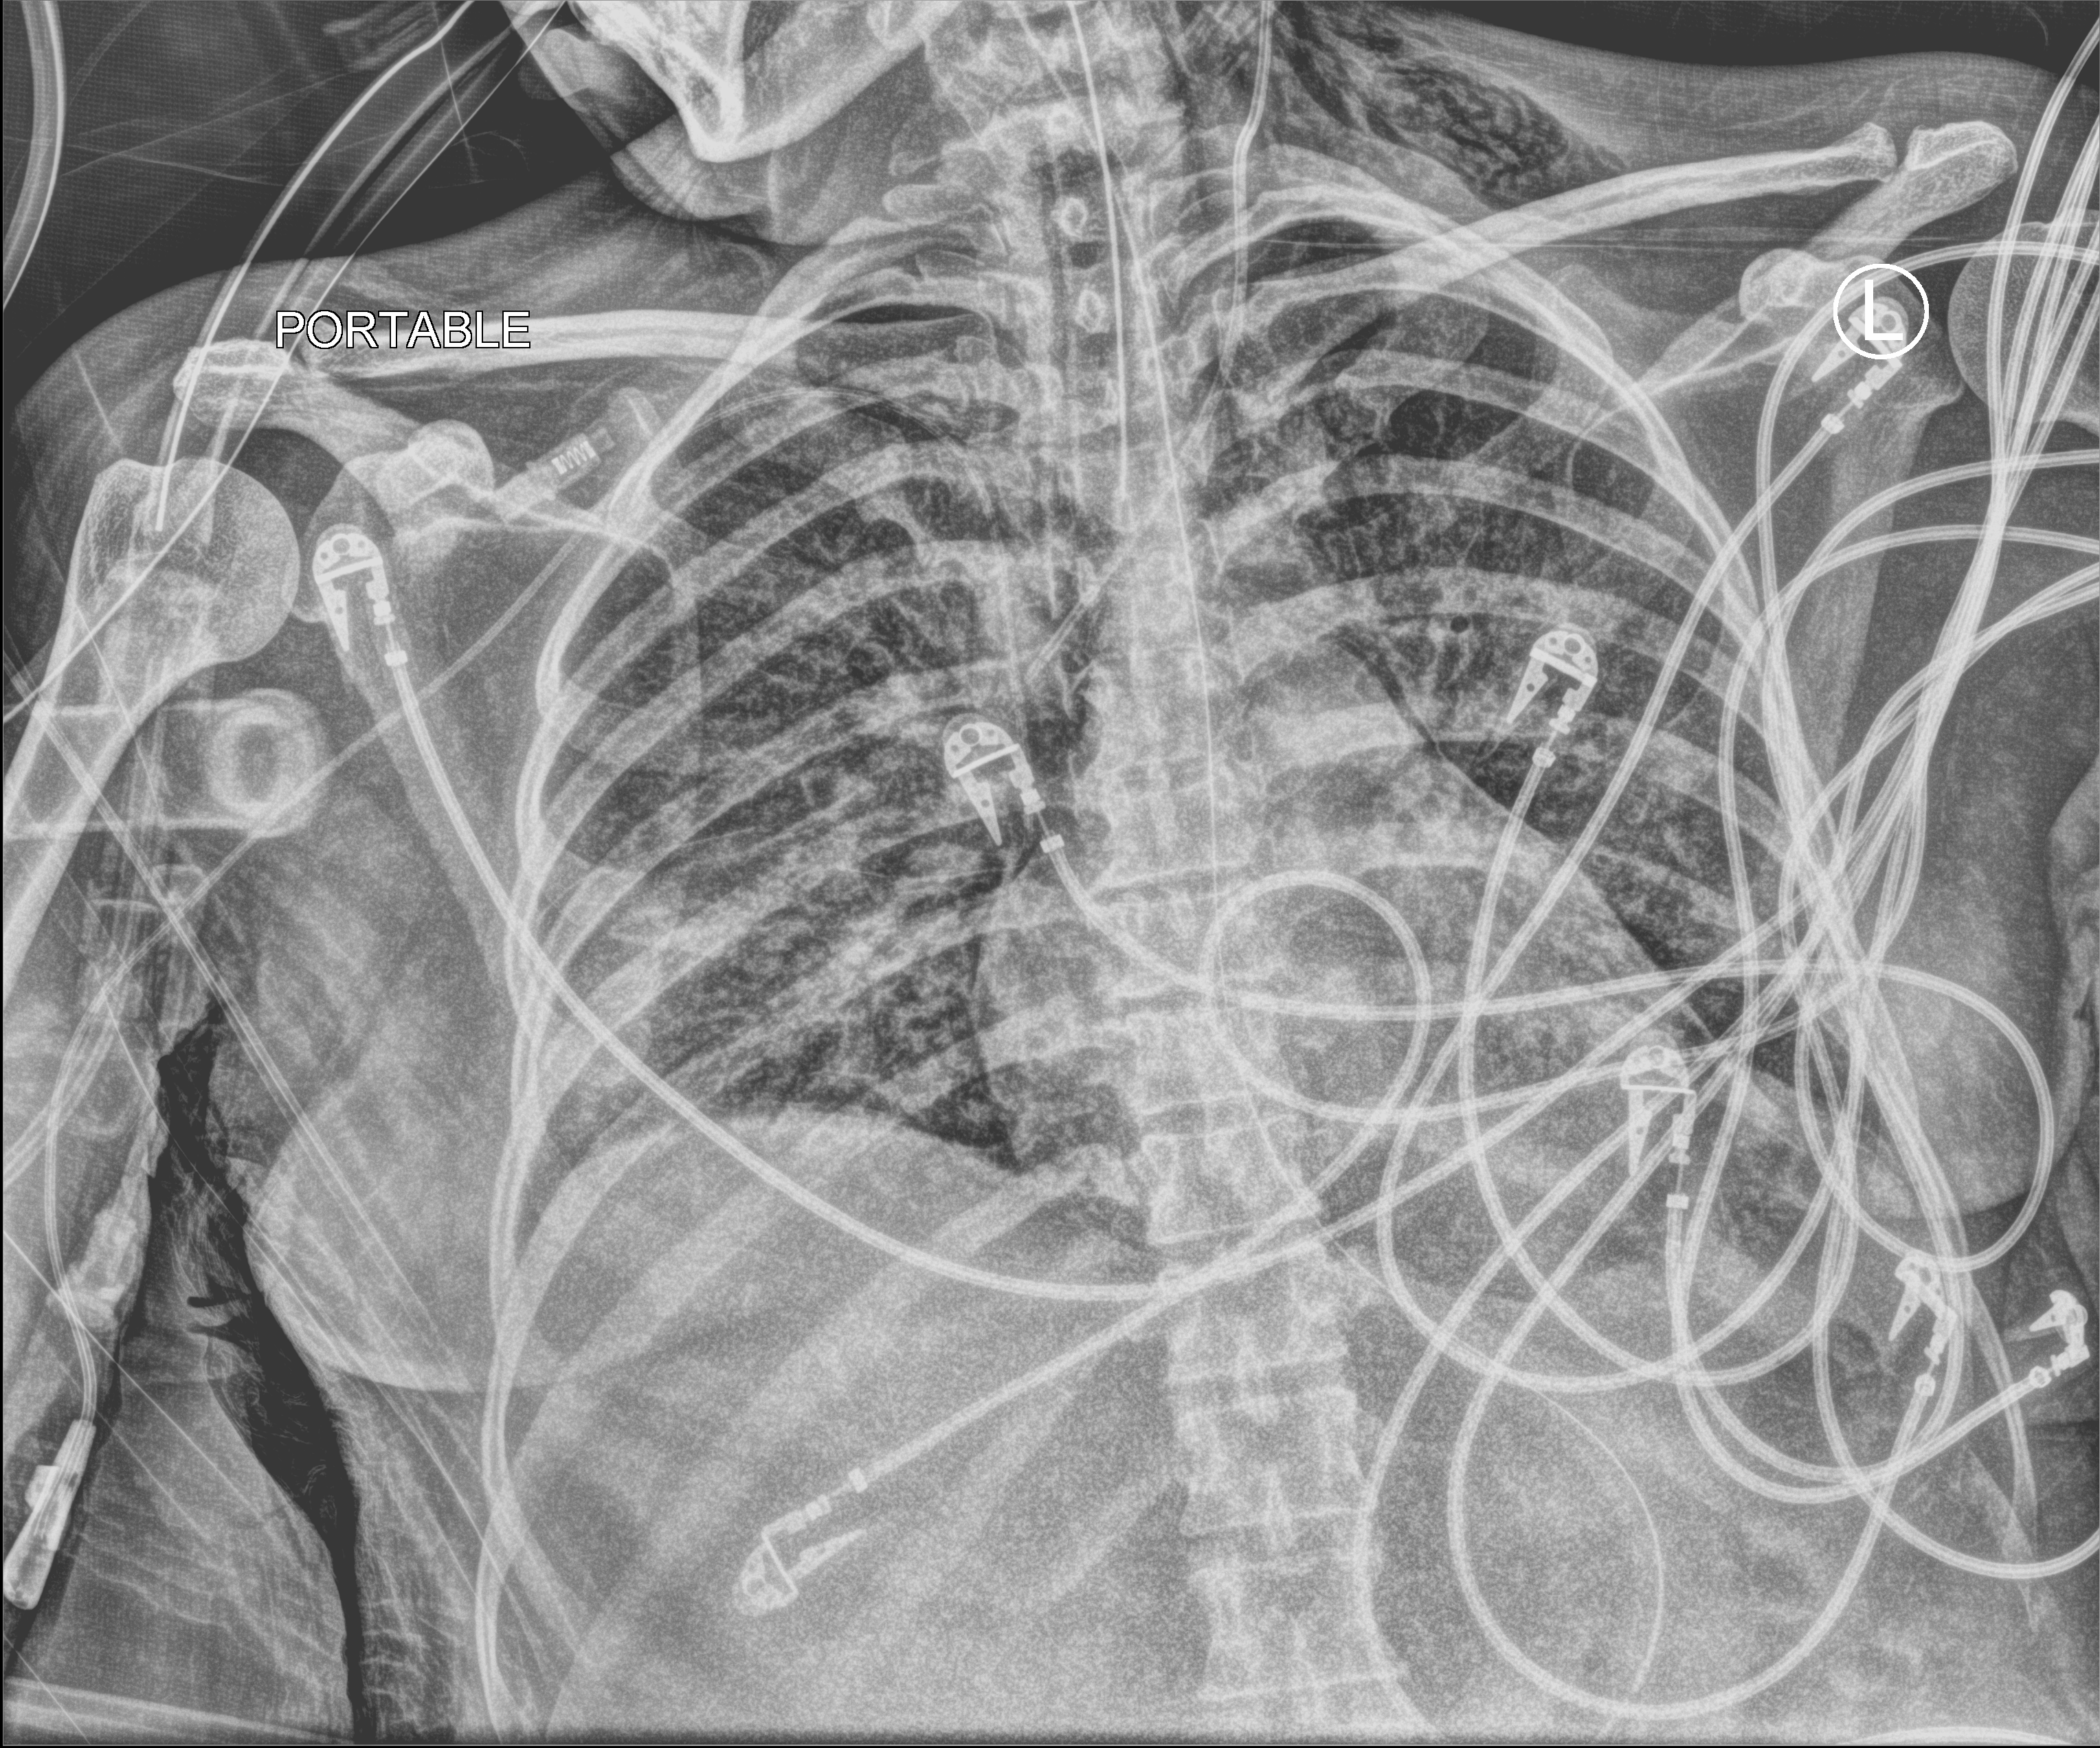
Portable chest radiograph. Female patient hospitalised with COVID-19, age 18–59 years.
Hospital-stay facts (about this admission, not read from this image; timing relative to this image not recorded): length of hospital stay: 71 days; chronic kidney disease (admission record): no; smoking status (admission record): former.